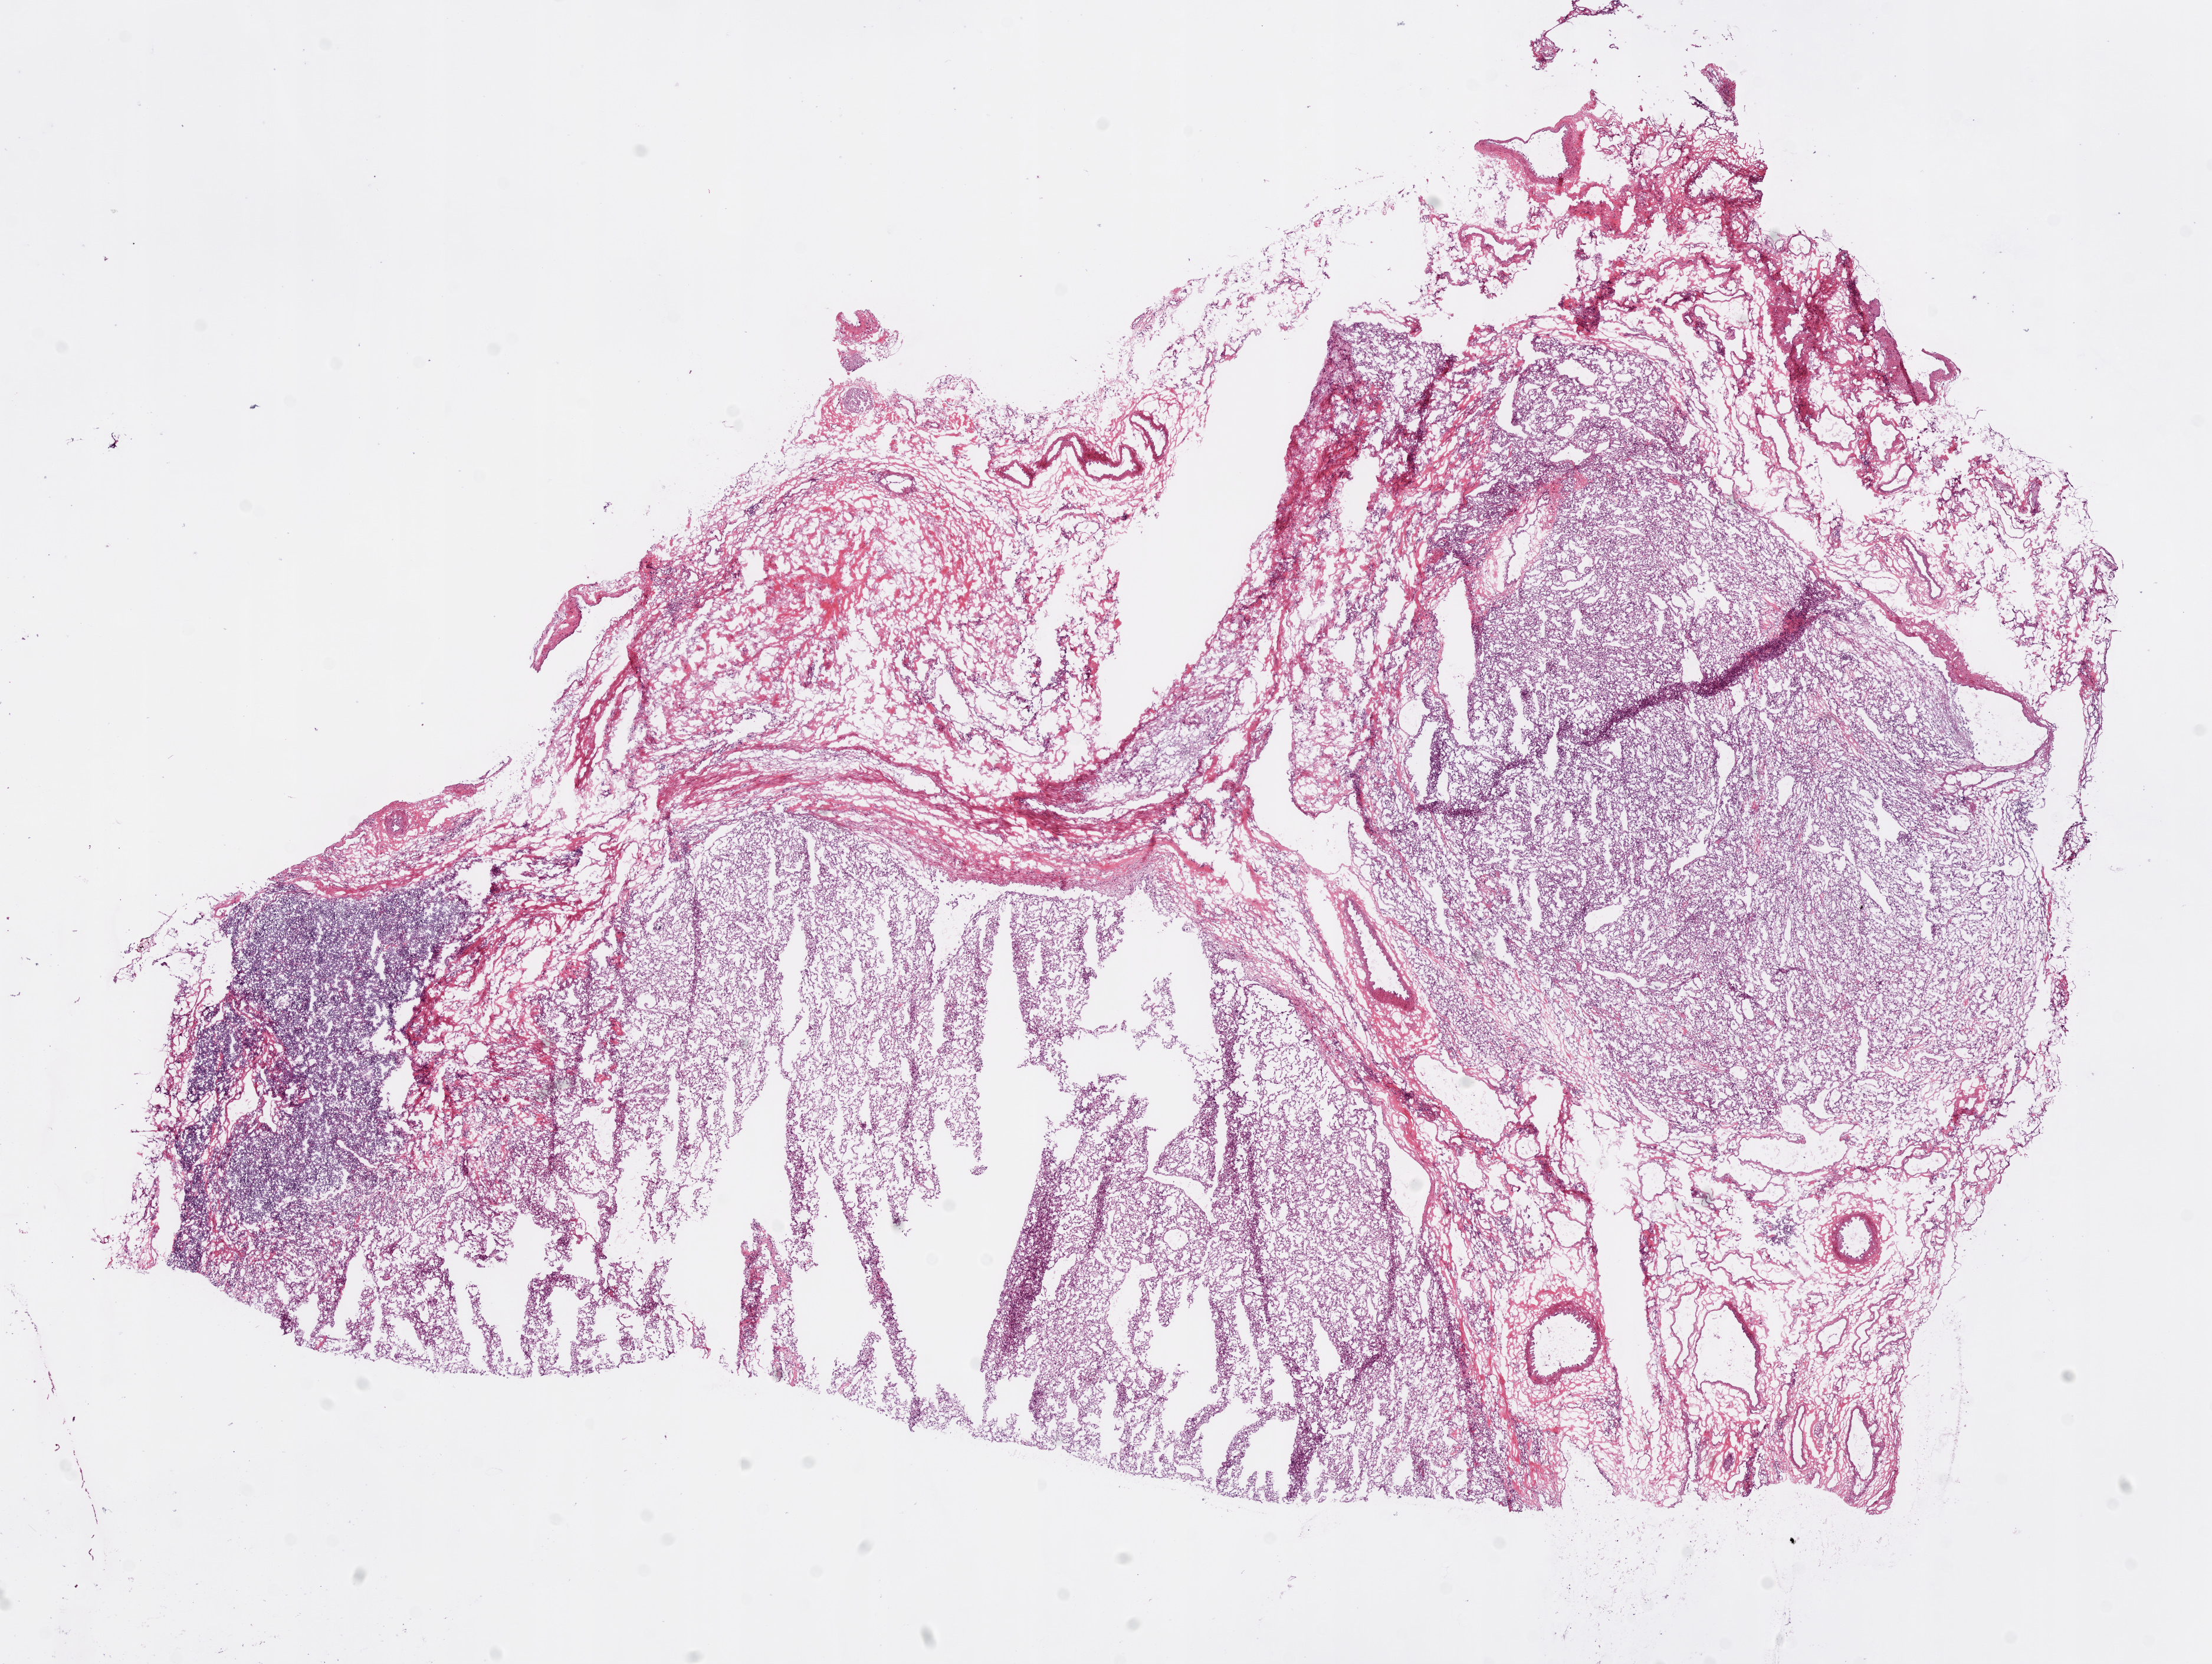
Digitized H&E-stained tissue section (whole slide), whole scanned area (about 15.0 x 11.3 mm, slide scanned at 20x) shown as a low-resolution overview, frozen section from the bottom of the tissue portion, primary tumour sample from the kidney. Male, age 63 years at initial diagnosis. Histologic grade: G4 (undifferentiated). Pathologist review of this section (percent, as recorded): tumour cells 80%, tumour nuclei 70%, normal cells 0%, stromal cells 20%, necrosis 0%.
• lymph nodes positive (case pathology): 0 of 15 examined
• AJCC pathologic stage: III
• diagnosis: Clear cell adenocarcinoma, NOS